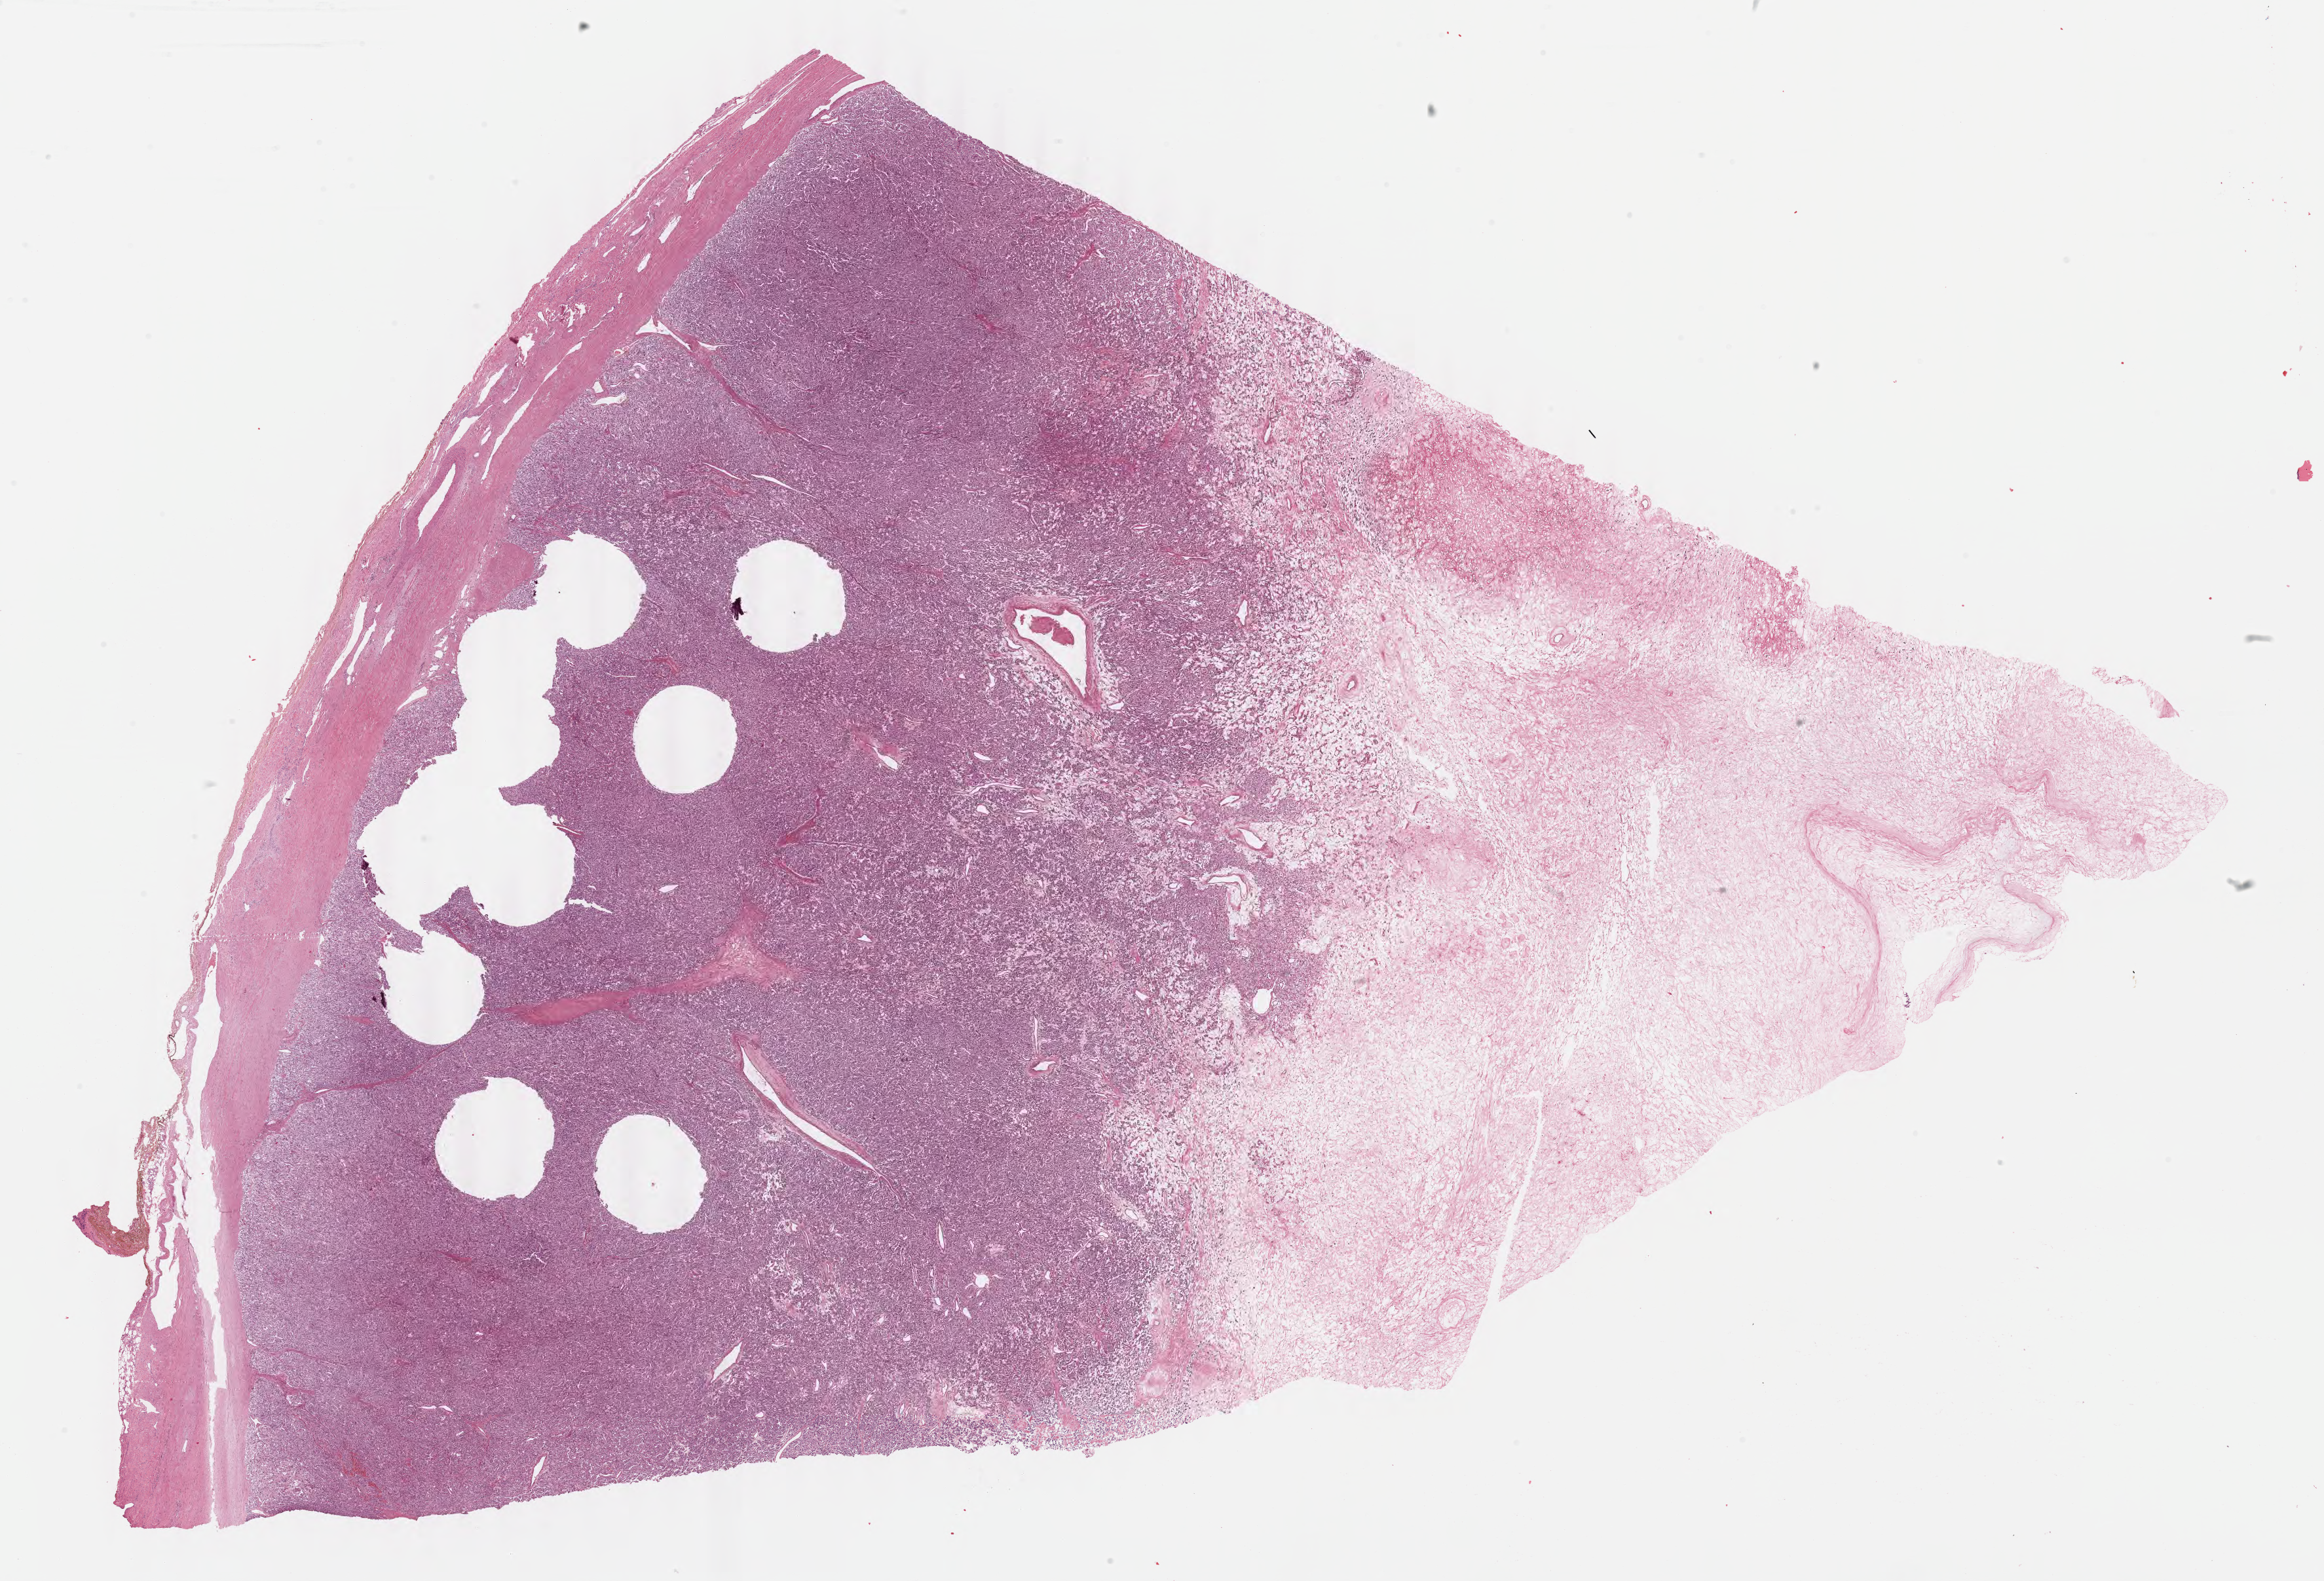
Whole-slide histology image, Hematoxylin and eosin (H&E) stained — whole scanned area (about 28.0 x 19.1 mm, from a 40x scan) shown as a low-resolution overview. Formalin-fixed paraffin-embedded (FFPE) diagnostic section. Adrenal gland, primary tumour sample. Female, age 35 years at initial diagnosis.
Histologic diagnosis: Carcinoid tumor, NOS (pancreas, NOS).